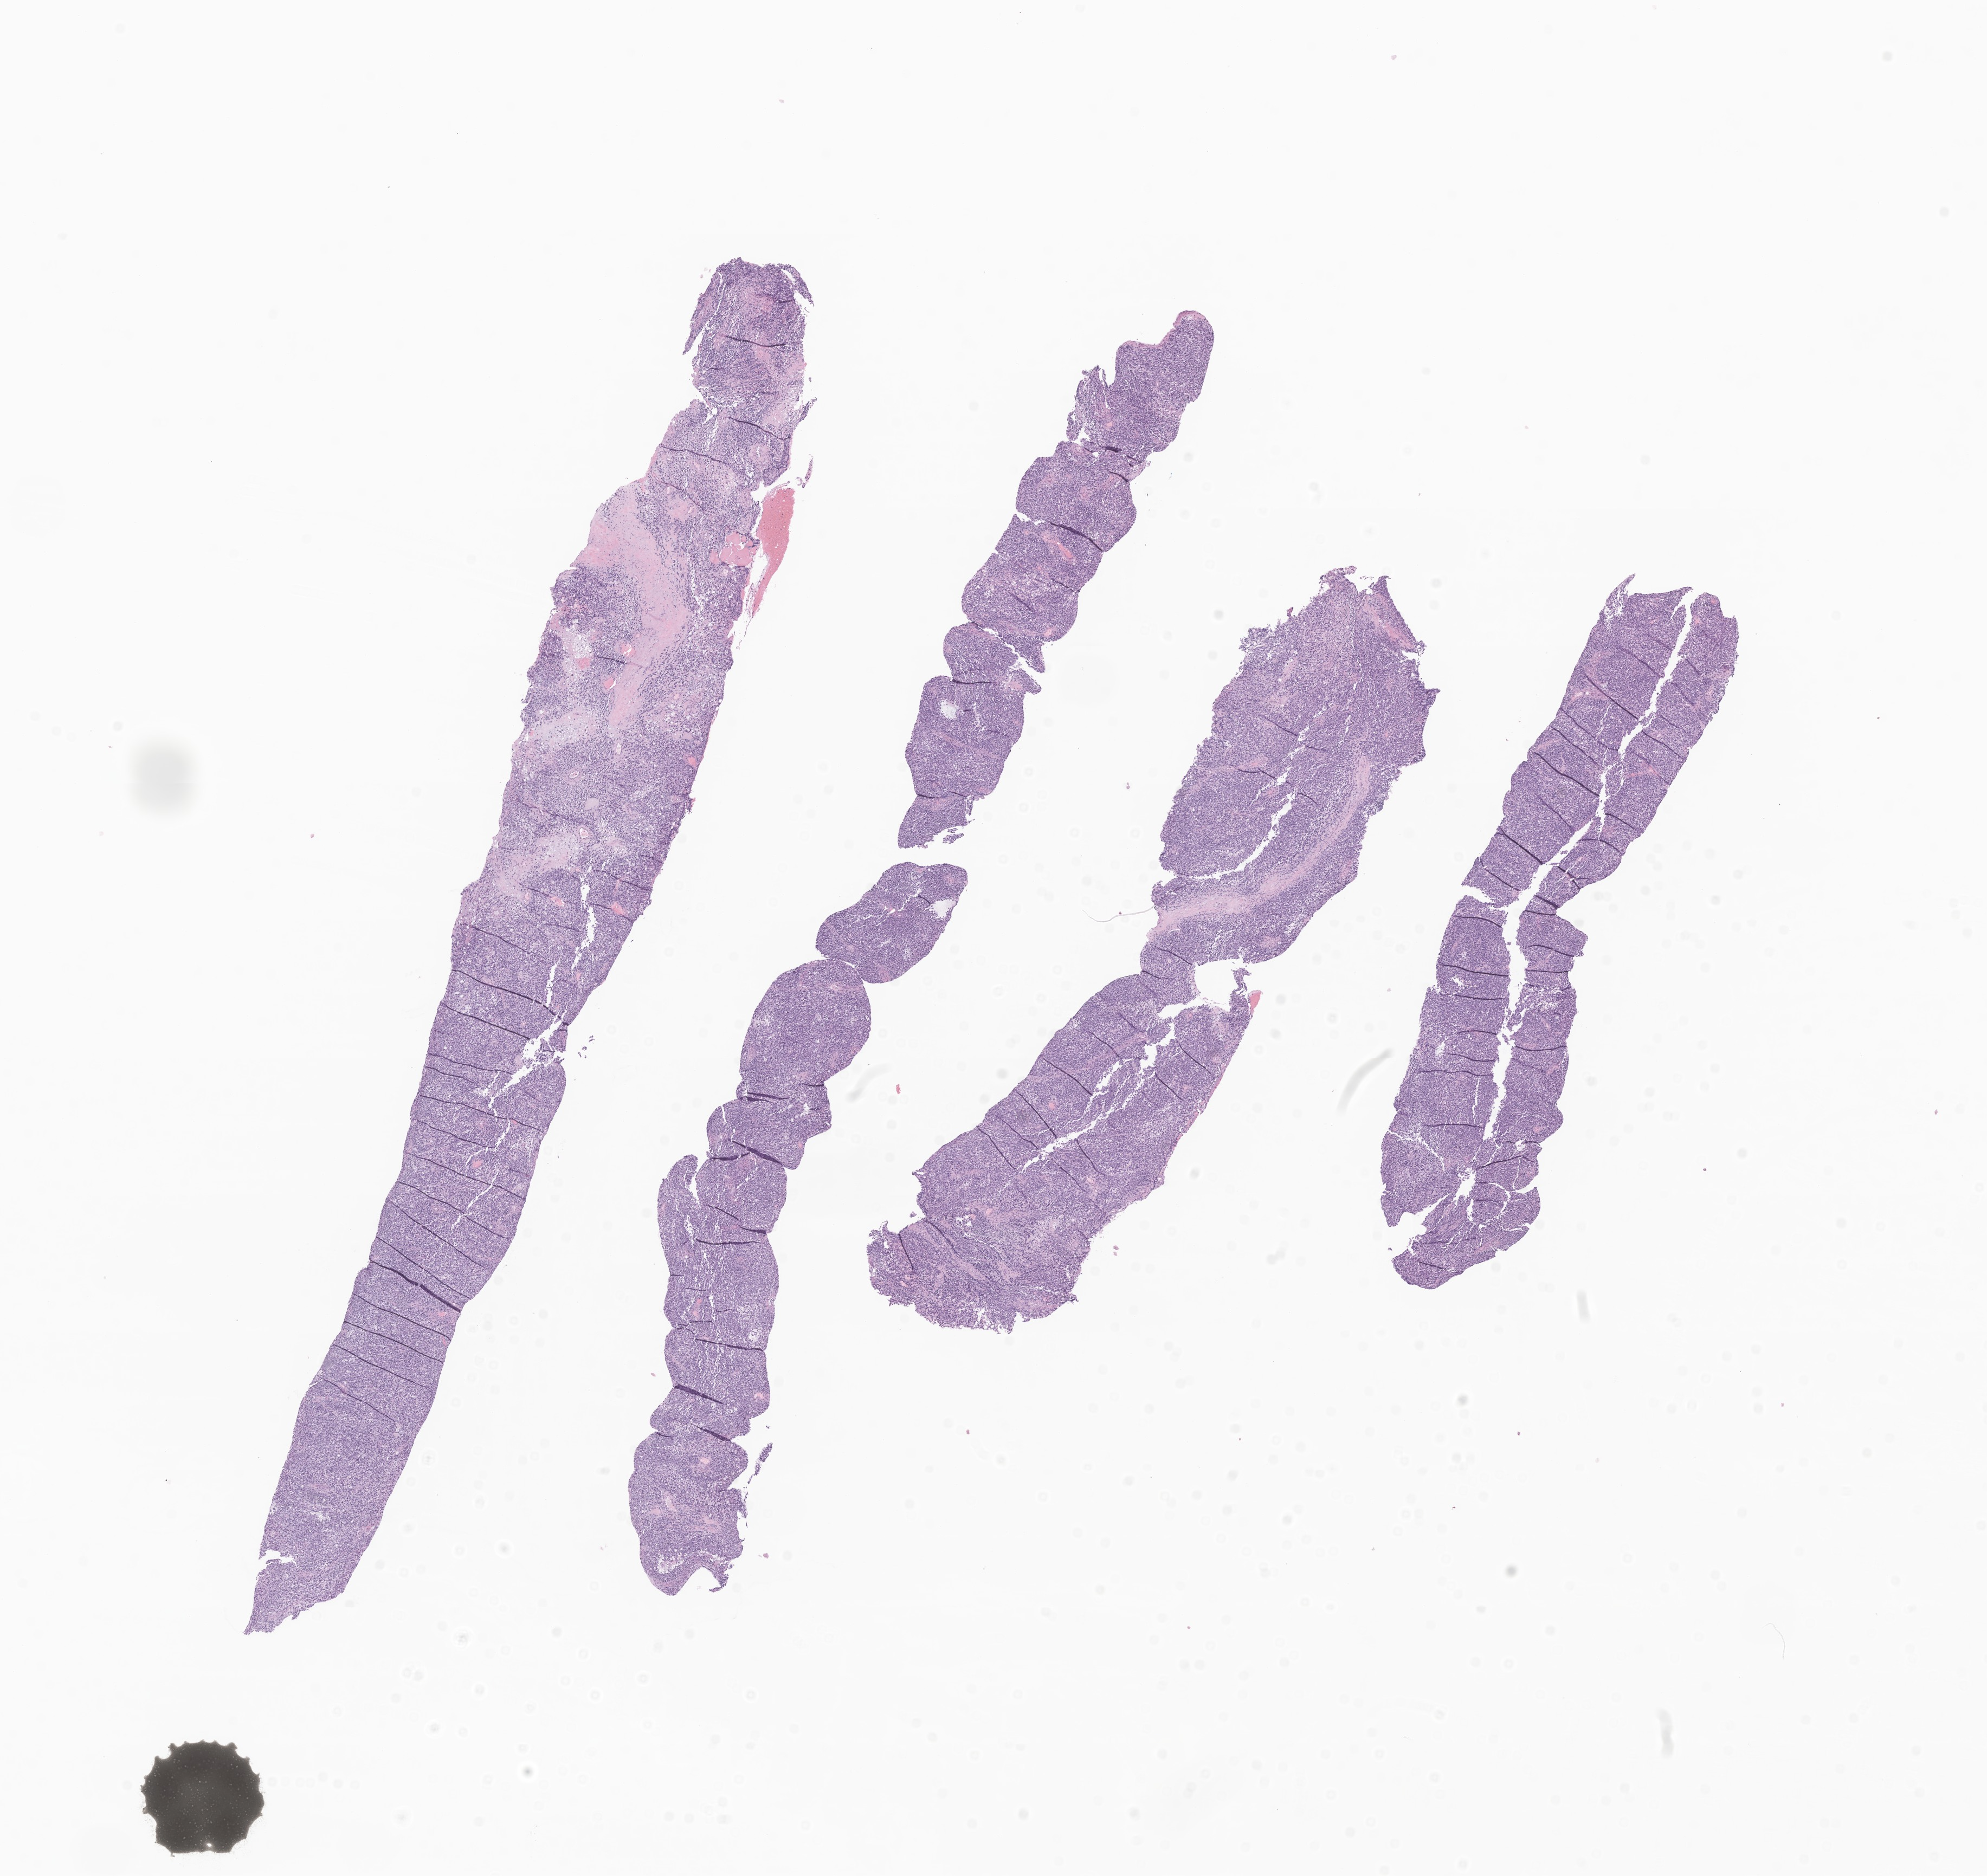
Whole-slide image, H&E stain of tumor tissue from the soft tissue, a low-resolution overview of the entire scanned area, about 15.5 x 14.6 mm, FFPE section. Patient male; age 128 months (10 years 8 months).
Diagnosis: Embryonal rhabdomyosarcoma, NOS.